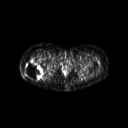
FDG PET of an extremity soft-tissue mass (from a PET/CT study), one axial slice; slice 39 of 267 in the series (ordered by position); 3.27 mm slice thickness; 128 × 128 image matrix. Patient: female, 57 years. Case-level facts recorded for this patient, not image findings: histological type: epithelioid sarcoma with vascular differentiation; site of the primary tumour: right buttock.
Structures marked on this image (expert contour drawn on MRI and transferred to this co-registered scan by the dataset authors):
- gross tumour volume (mass): bounding box <24,60,44,80> (left, top, right, bottom; pixels)